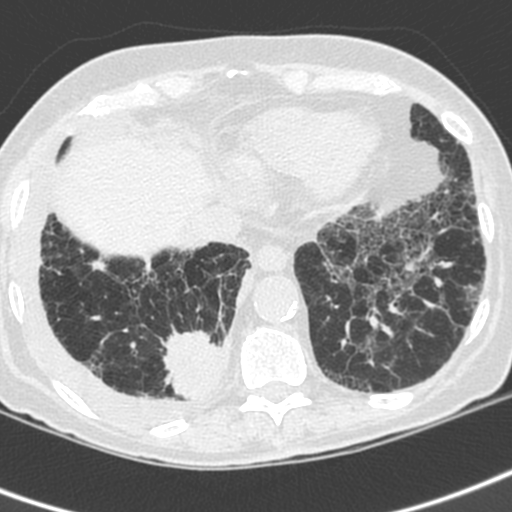
Low-dose screening chest CT, axial slice, baseline screening round, lung window (W 1500 / L -600 HU), 1.3 mm slice thickness, standard (soft-tissue) reconstruction kernel (C), slice 147 of 192 in the series. Female, age 73 years at enrolment.
- Lesion marked by an expert reader, bounding box (x1, y1, x2, y2) in pixels: (158, 322, 235, 405).
- The exam's reader record, not a measurement of the box and not confirmed to be the same lesion: non-calcified nodule or mass ≥4 mm, right lower lobe, 35 × 30 mm, spiculated (stellate) margins, soft tissue attenuation.
- Participant outcome: lung cancer diagnosed 22 days after this screen — adenocarcinoma, NOS, right lower lobe, stage IV (AJCC 6th edition), 35 mm at pathology.